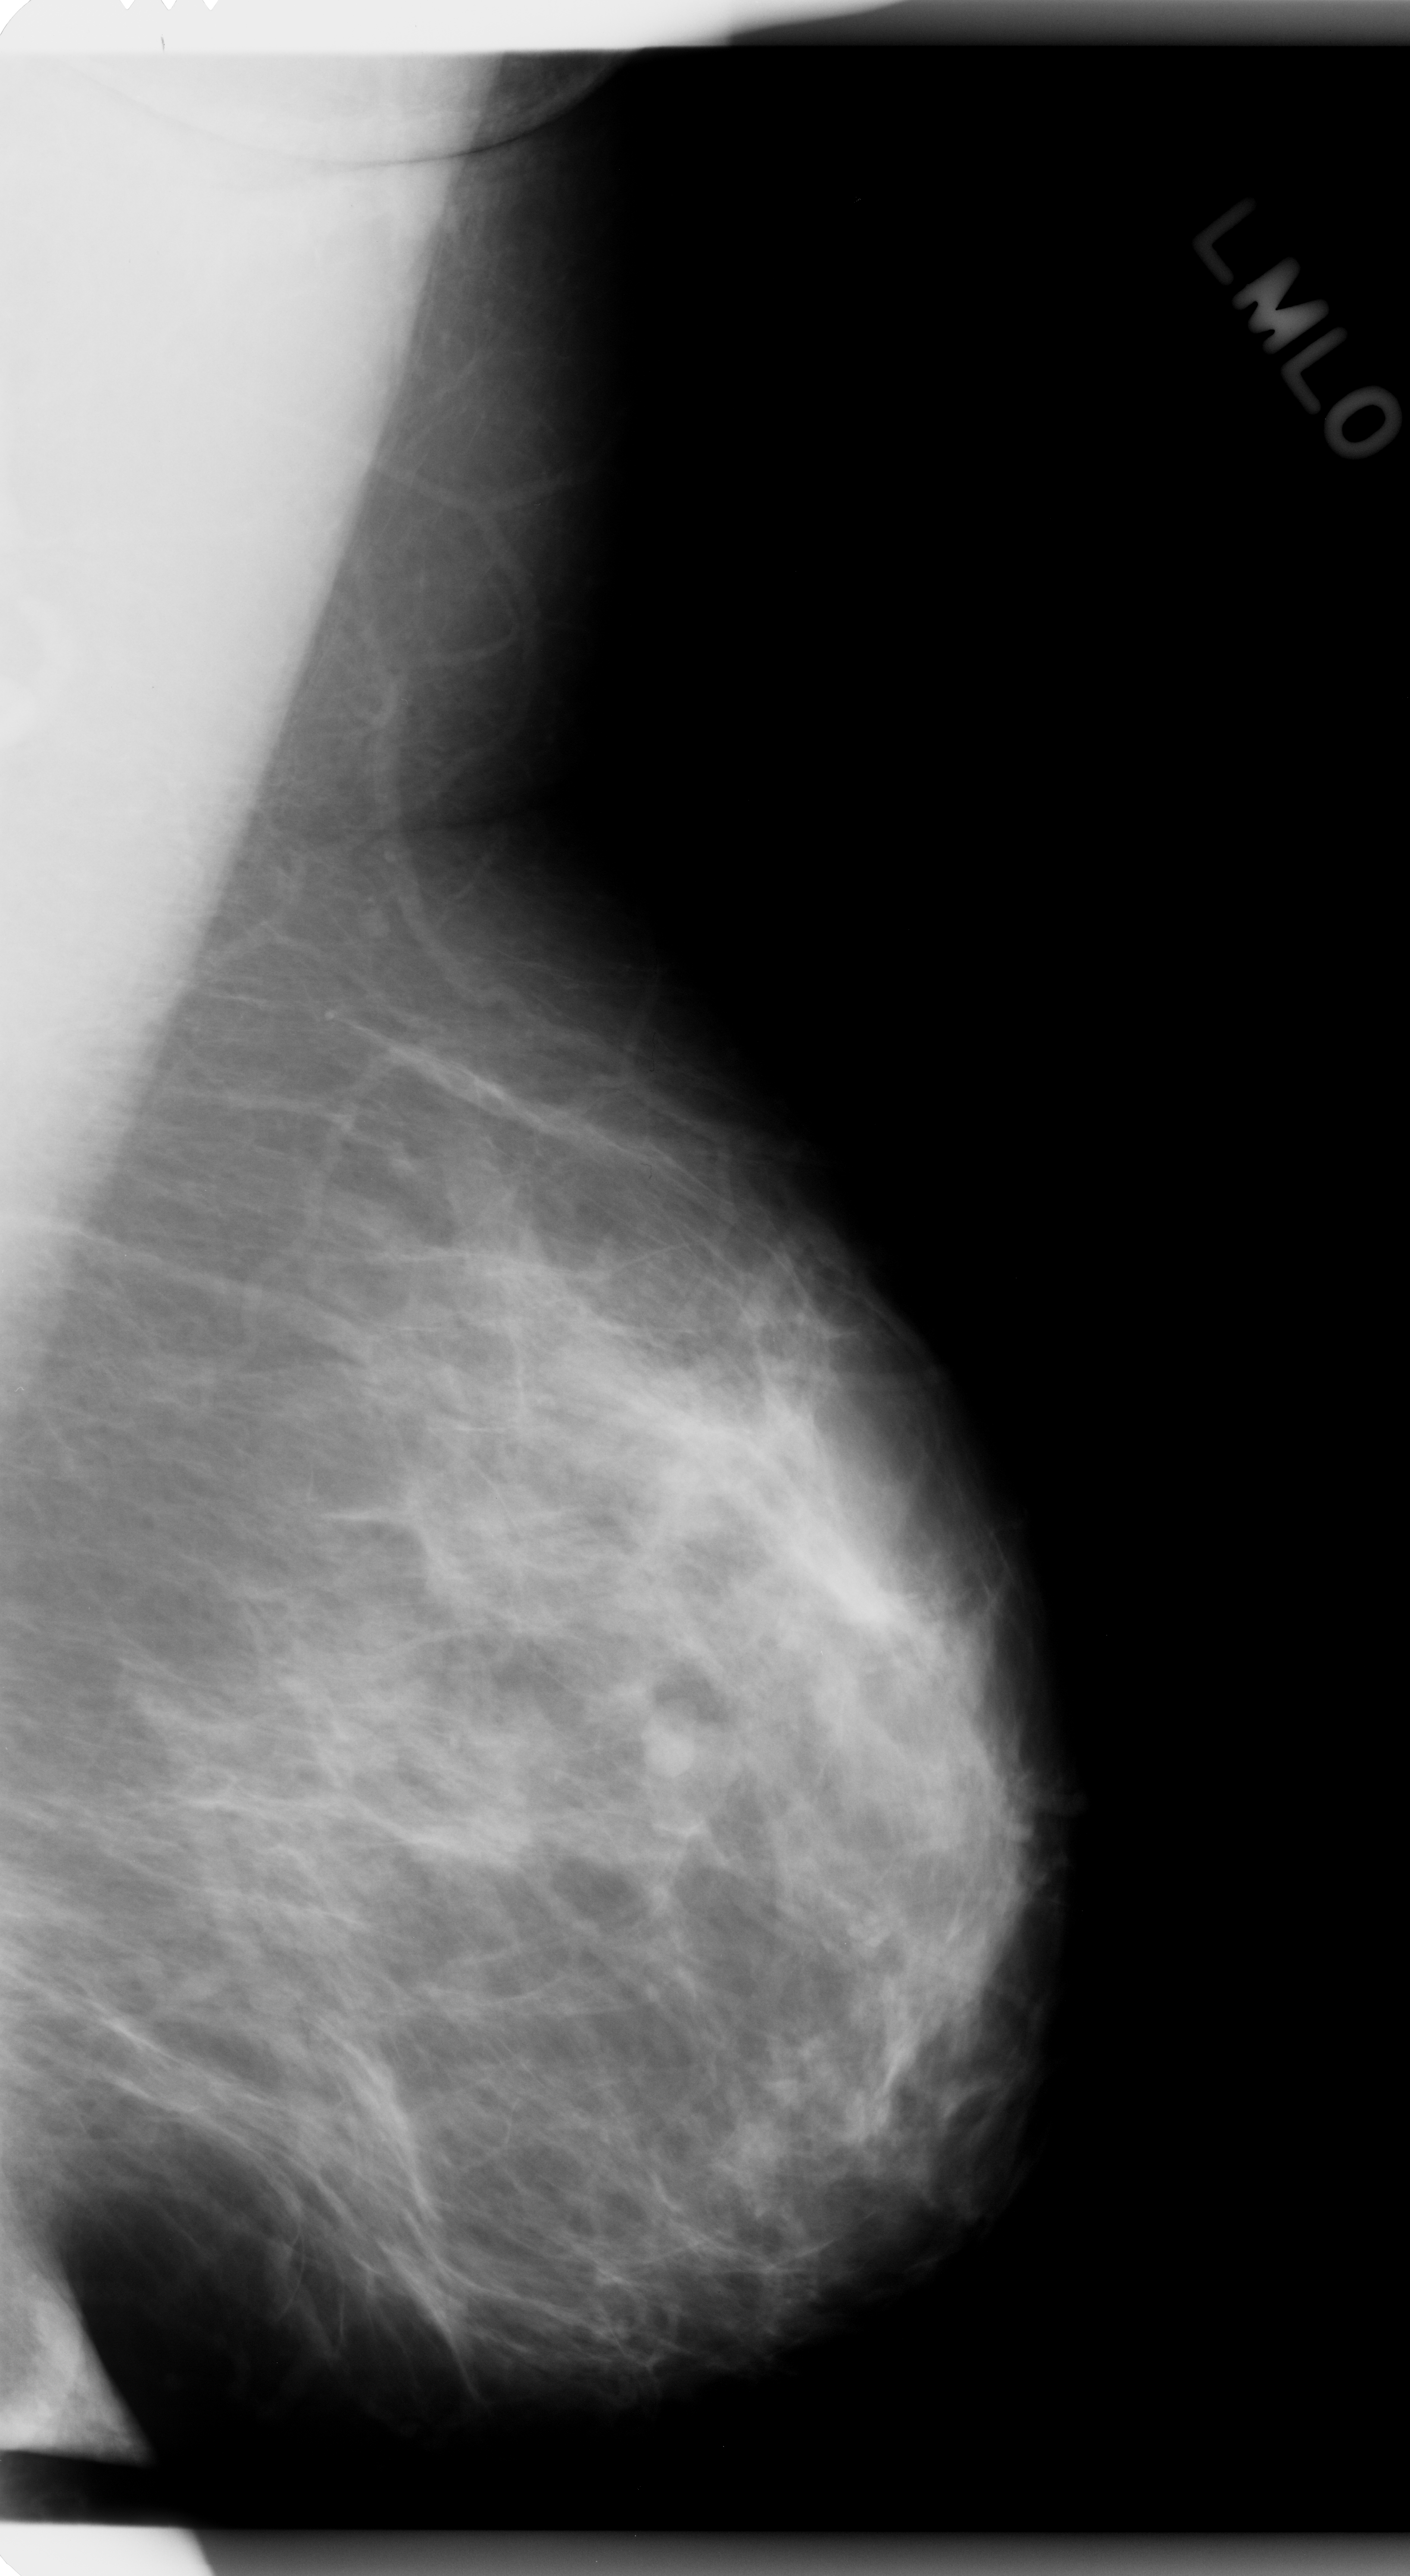
Scanned film-screen mammogram, left breast, mediolateral oblique (MLO) view.
- Abnormality record for this image: mass, shape lobulated, margins circumscribed; BI-RADS assessment category 3; pathology result (as recorded, not read from the image): benign.